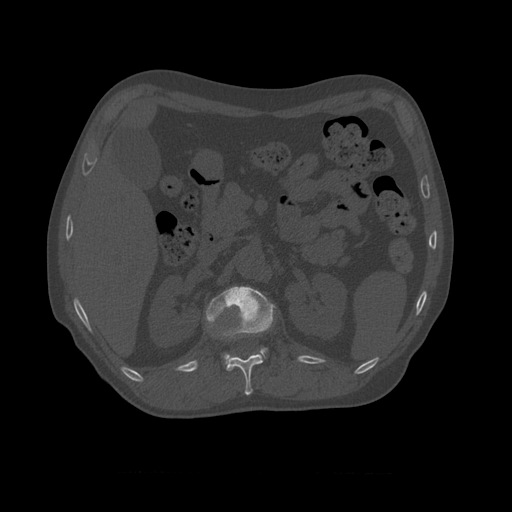
CT including the spine, one axial slice. Position 369 of 450 along the scan axis. 120 kVp. Bone window (W 1800 / L 400 HU). 1.25 mm slice thickness. 512 × 512 image matrix, field of view 405 × 405 mm. Patient age 75 years. Case-level facts recorded for this patient, not image findings: primary cancer: prostate.
Structures marked on this image (semi-automatically segmented with operator editing):
- L1 vertebra: bounding box <206,287,276,365> (left, top, right, bottom; pixels)
- T10 vertebra: <259,347,268,359>
- T11 vertebra: <207,330,264,396>